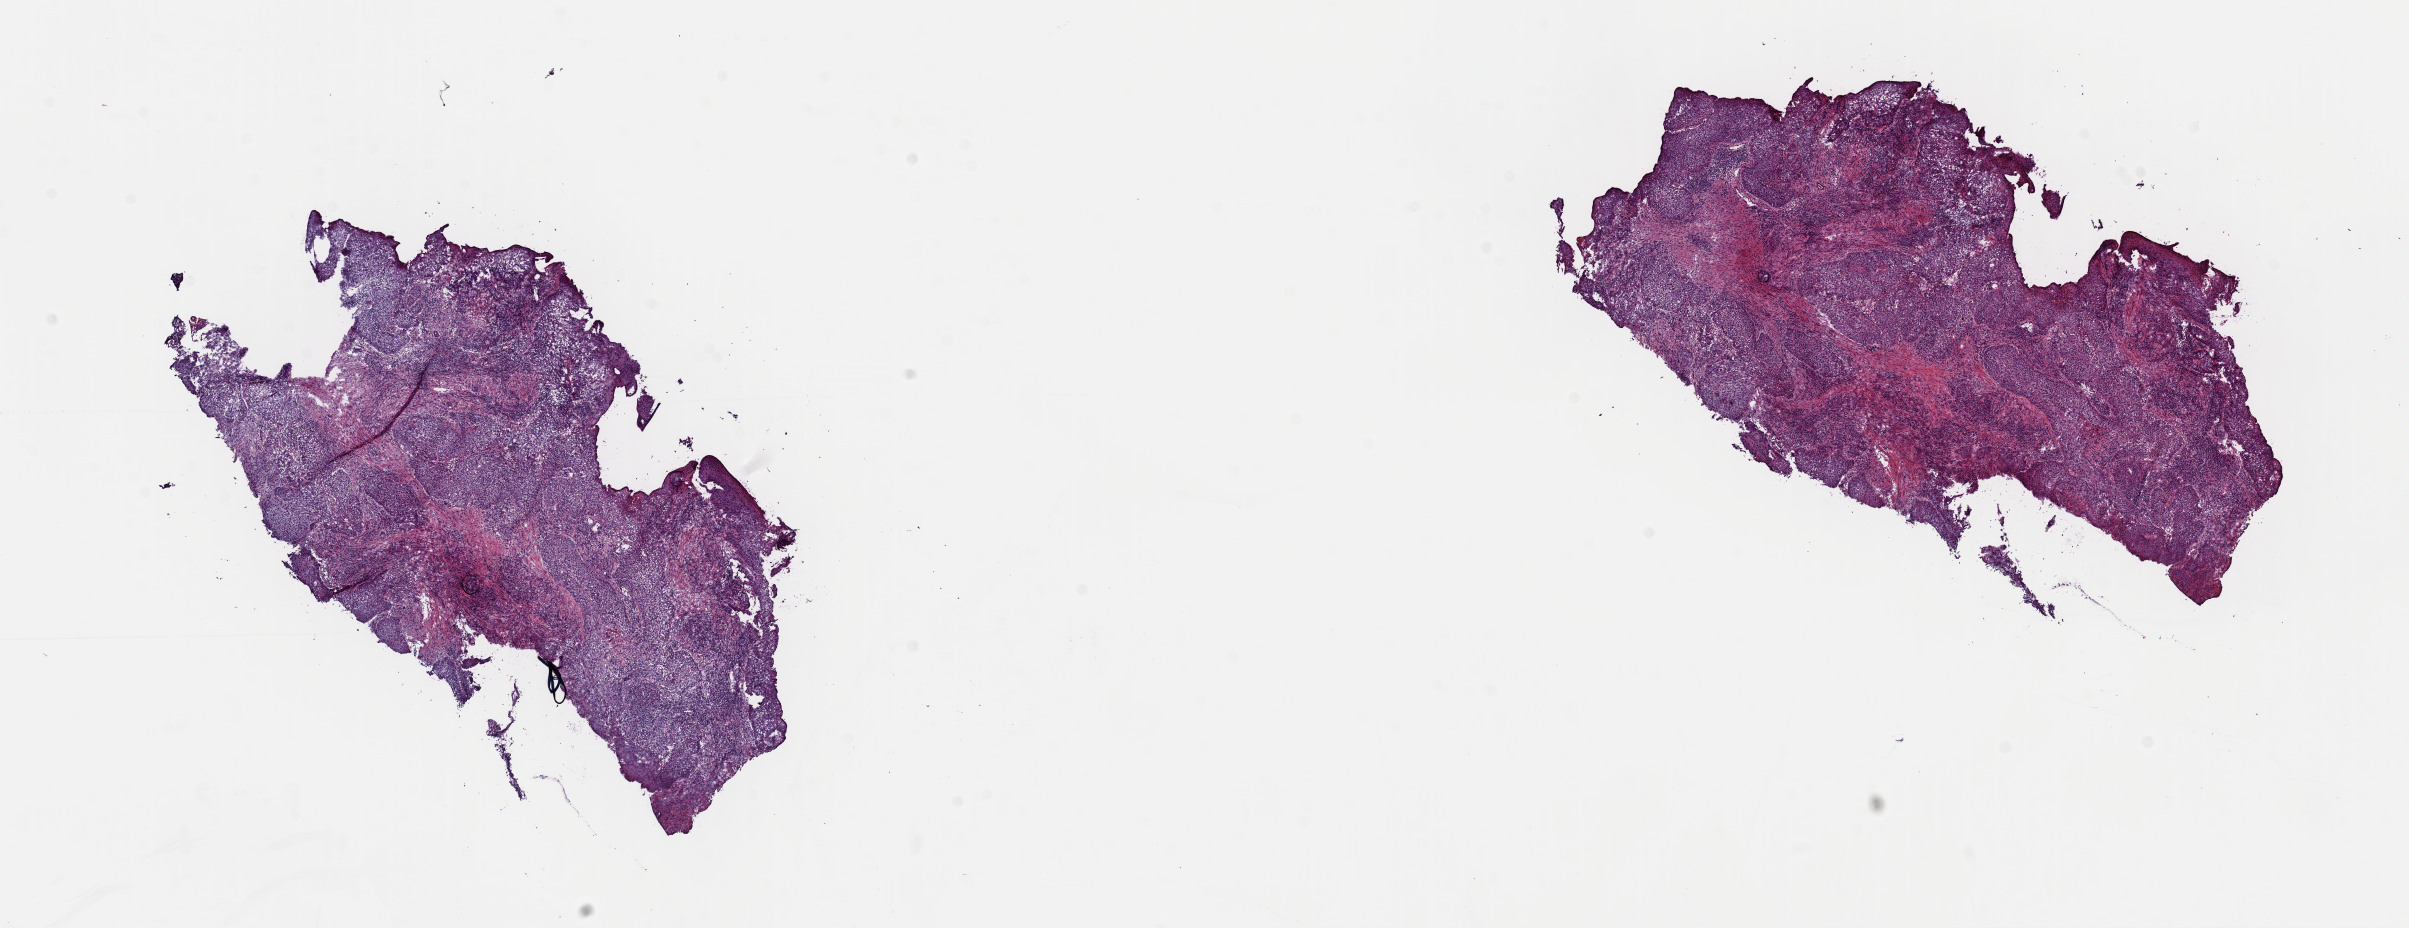
Digitized Hematoxylin and eosin (H&E) stained tissue section (whole slide) — shown as a low-resolution overview of the whole scanned area (about 19.0 x 7.3 mm, acquisition: 40x scan). Frozen section from the top of the tissue portion. Lung, primary tumour sample. Patient: male, age at initial diagnosis 67 years. Composition of this section per pathologist review: tumour cells 98%, tumour nuclei 80%, normal cells 0%, stromal cells 0%, necrosis 2%. Infiltration values recorded for this section: lymphocyte infiltration 2%, monocyte infiltration 0%, neutrophil infiltration 0%.
Histologic diagnosis: Squamous cell carcinoma, NOS. AJCC pathologic stage: IIB (7th edition).